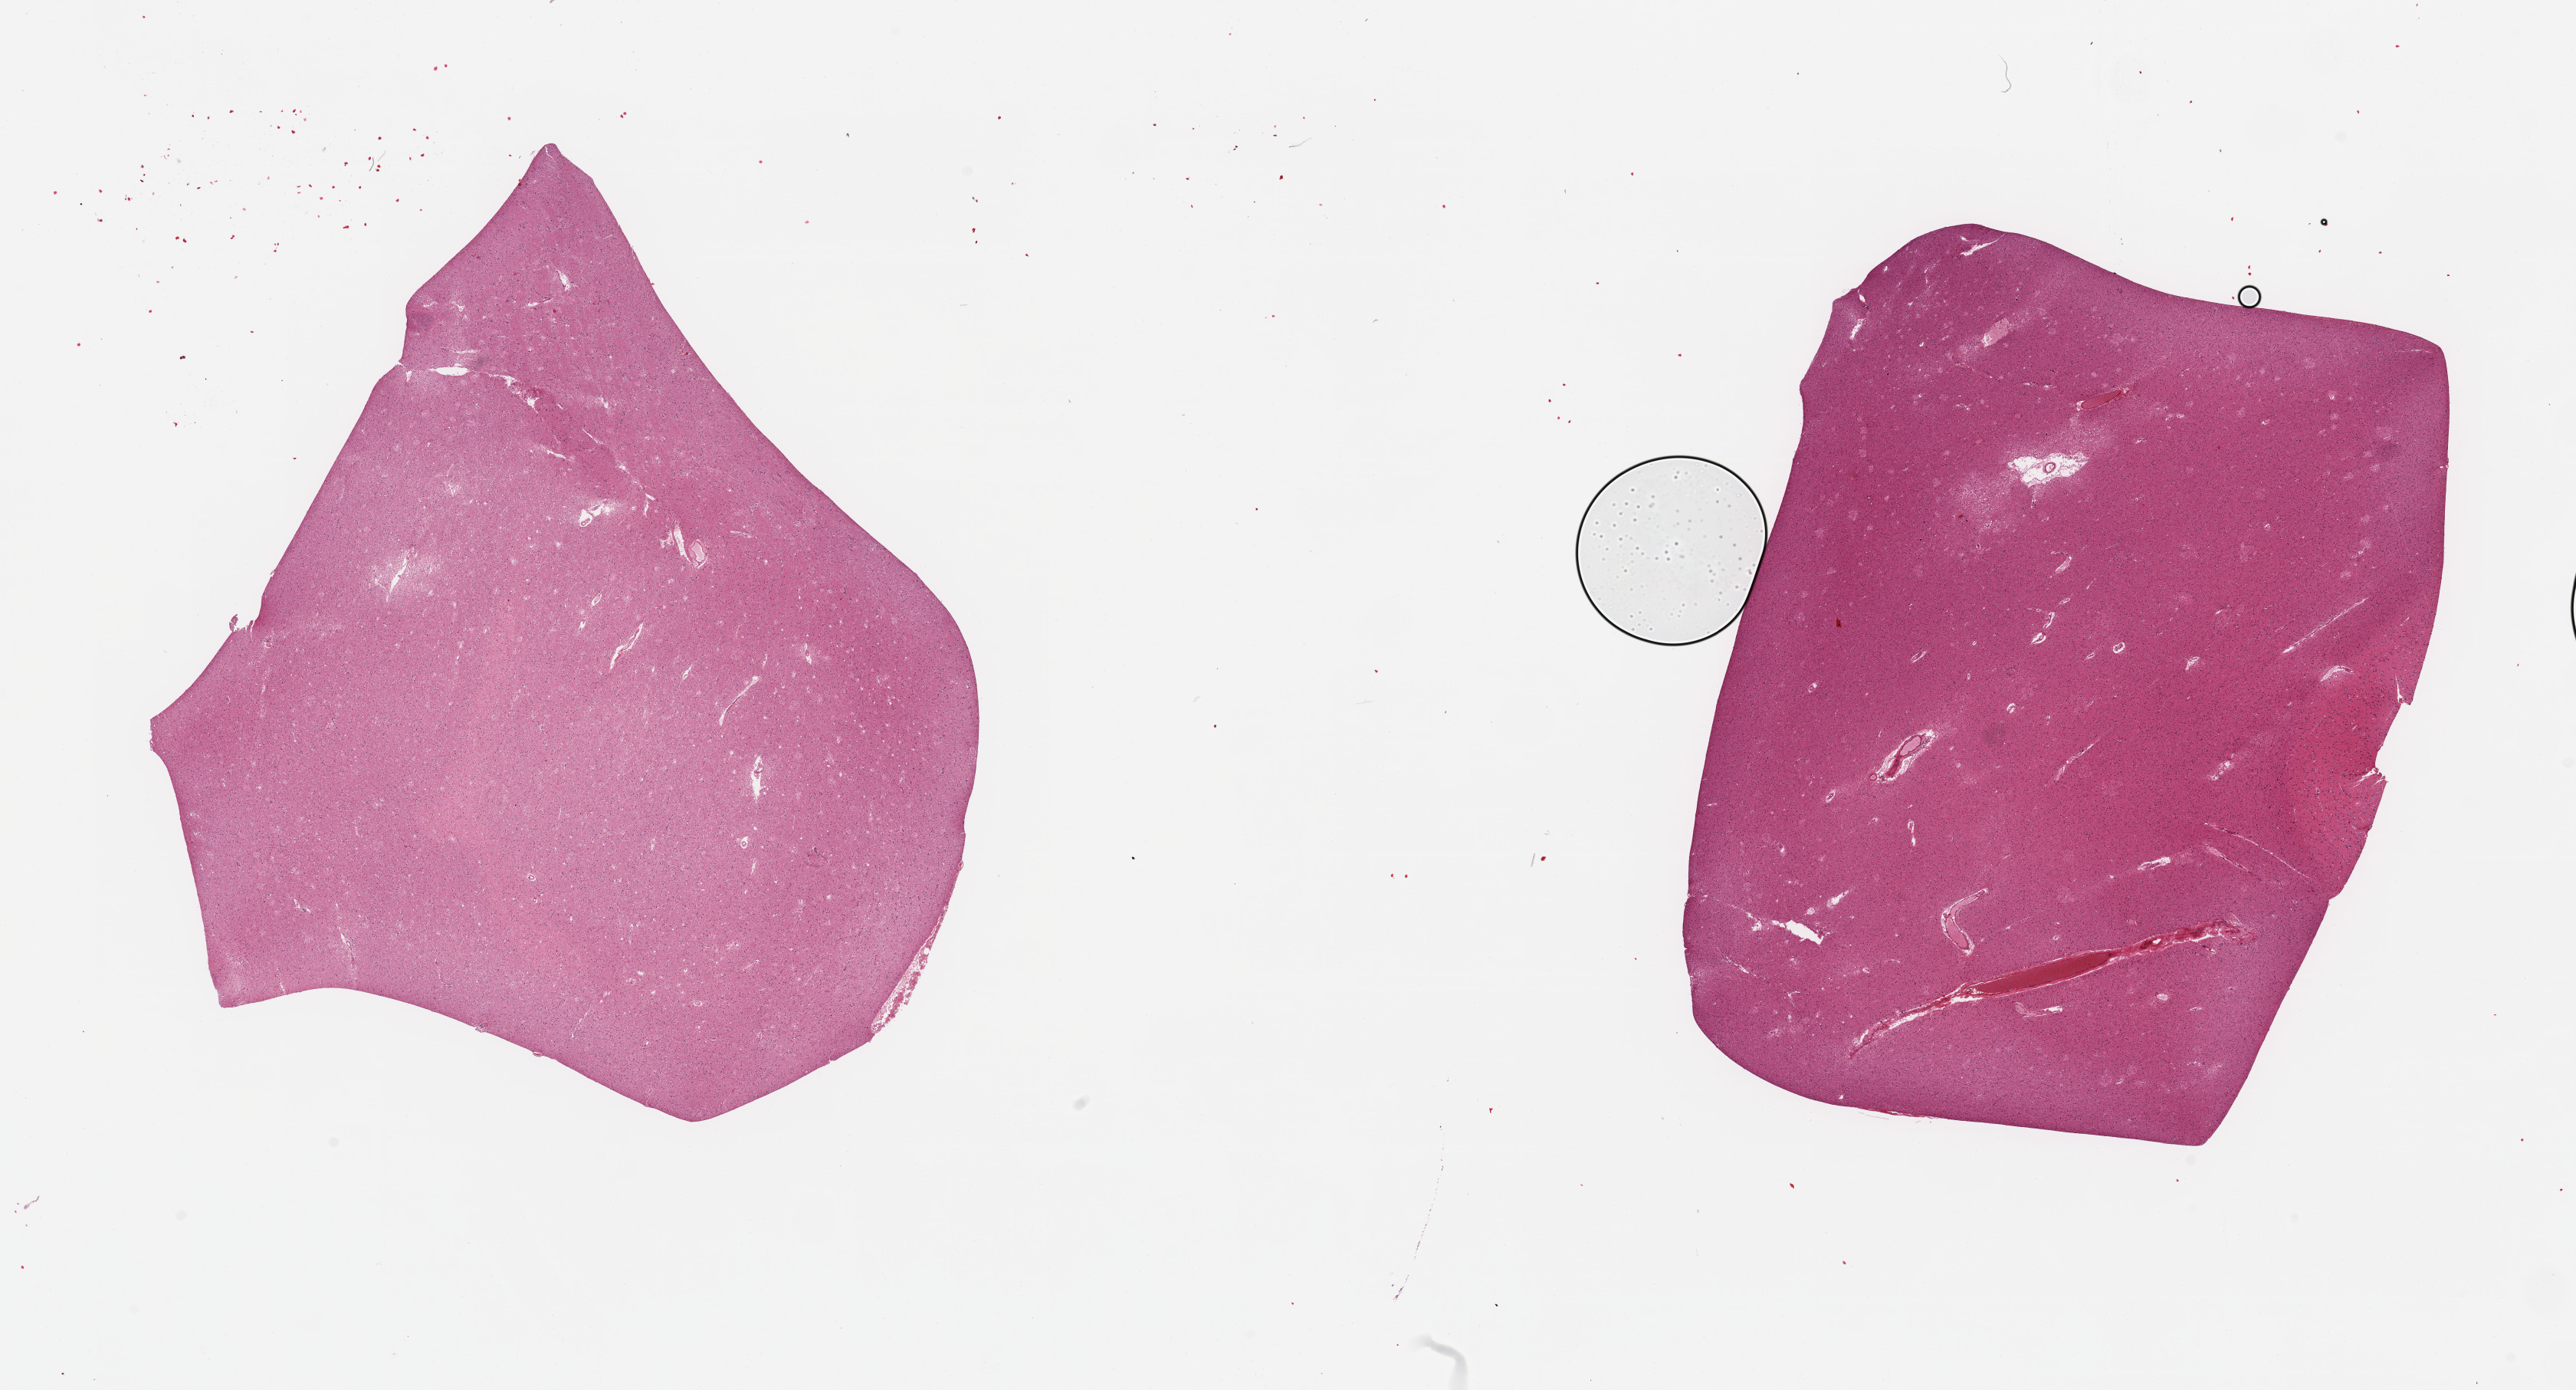
Haematoxylin and eosin whole-slide image, brightfield — whole scanned area (about 26.6 x 14.3 mm) shown as a low-resolution overview. PAXgene-fixed paraffin-embedded (PFPE) section. Sampled site (target tissue): cerebral cortex. Donor tissue sample. Donor sex: female.
* reviewer comment on this tissue sample: 2 pieces; excessive white matter compared to gray